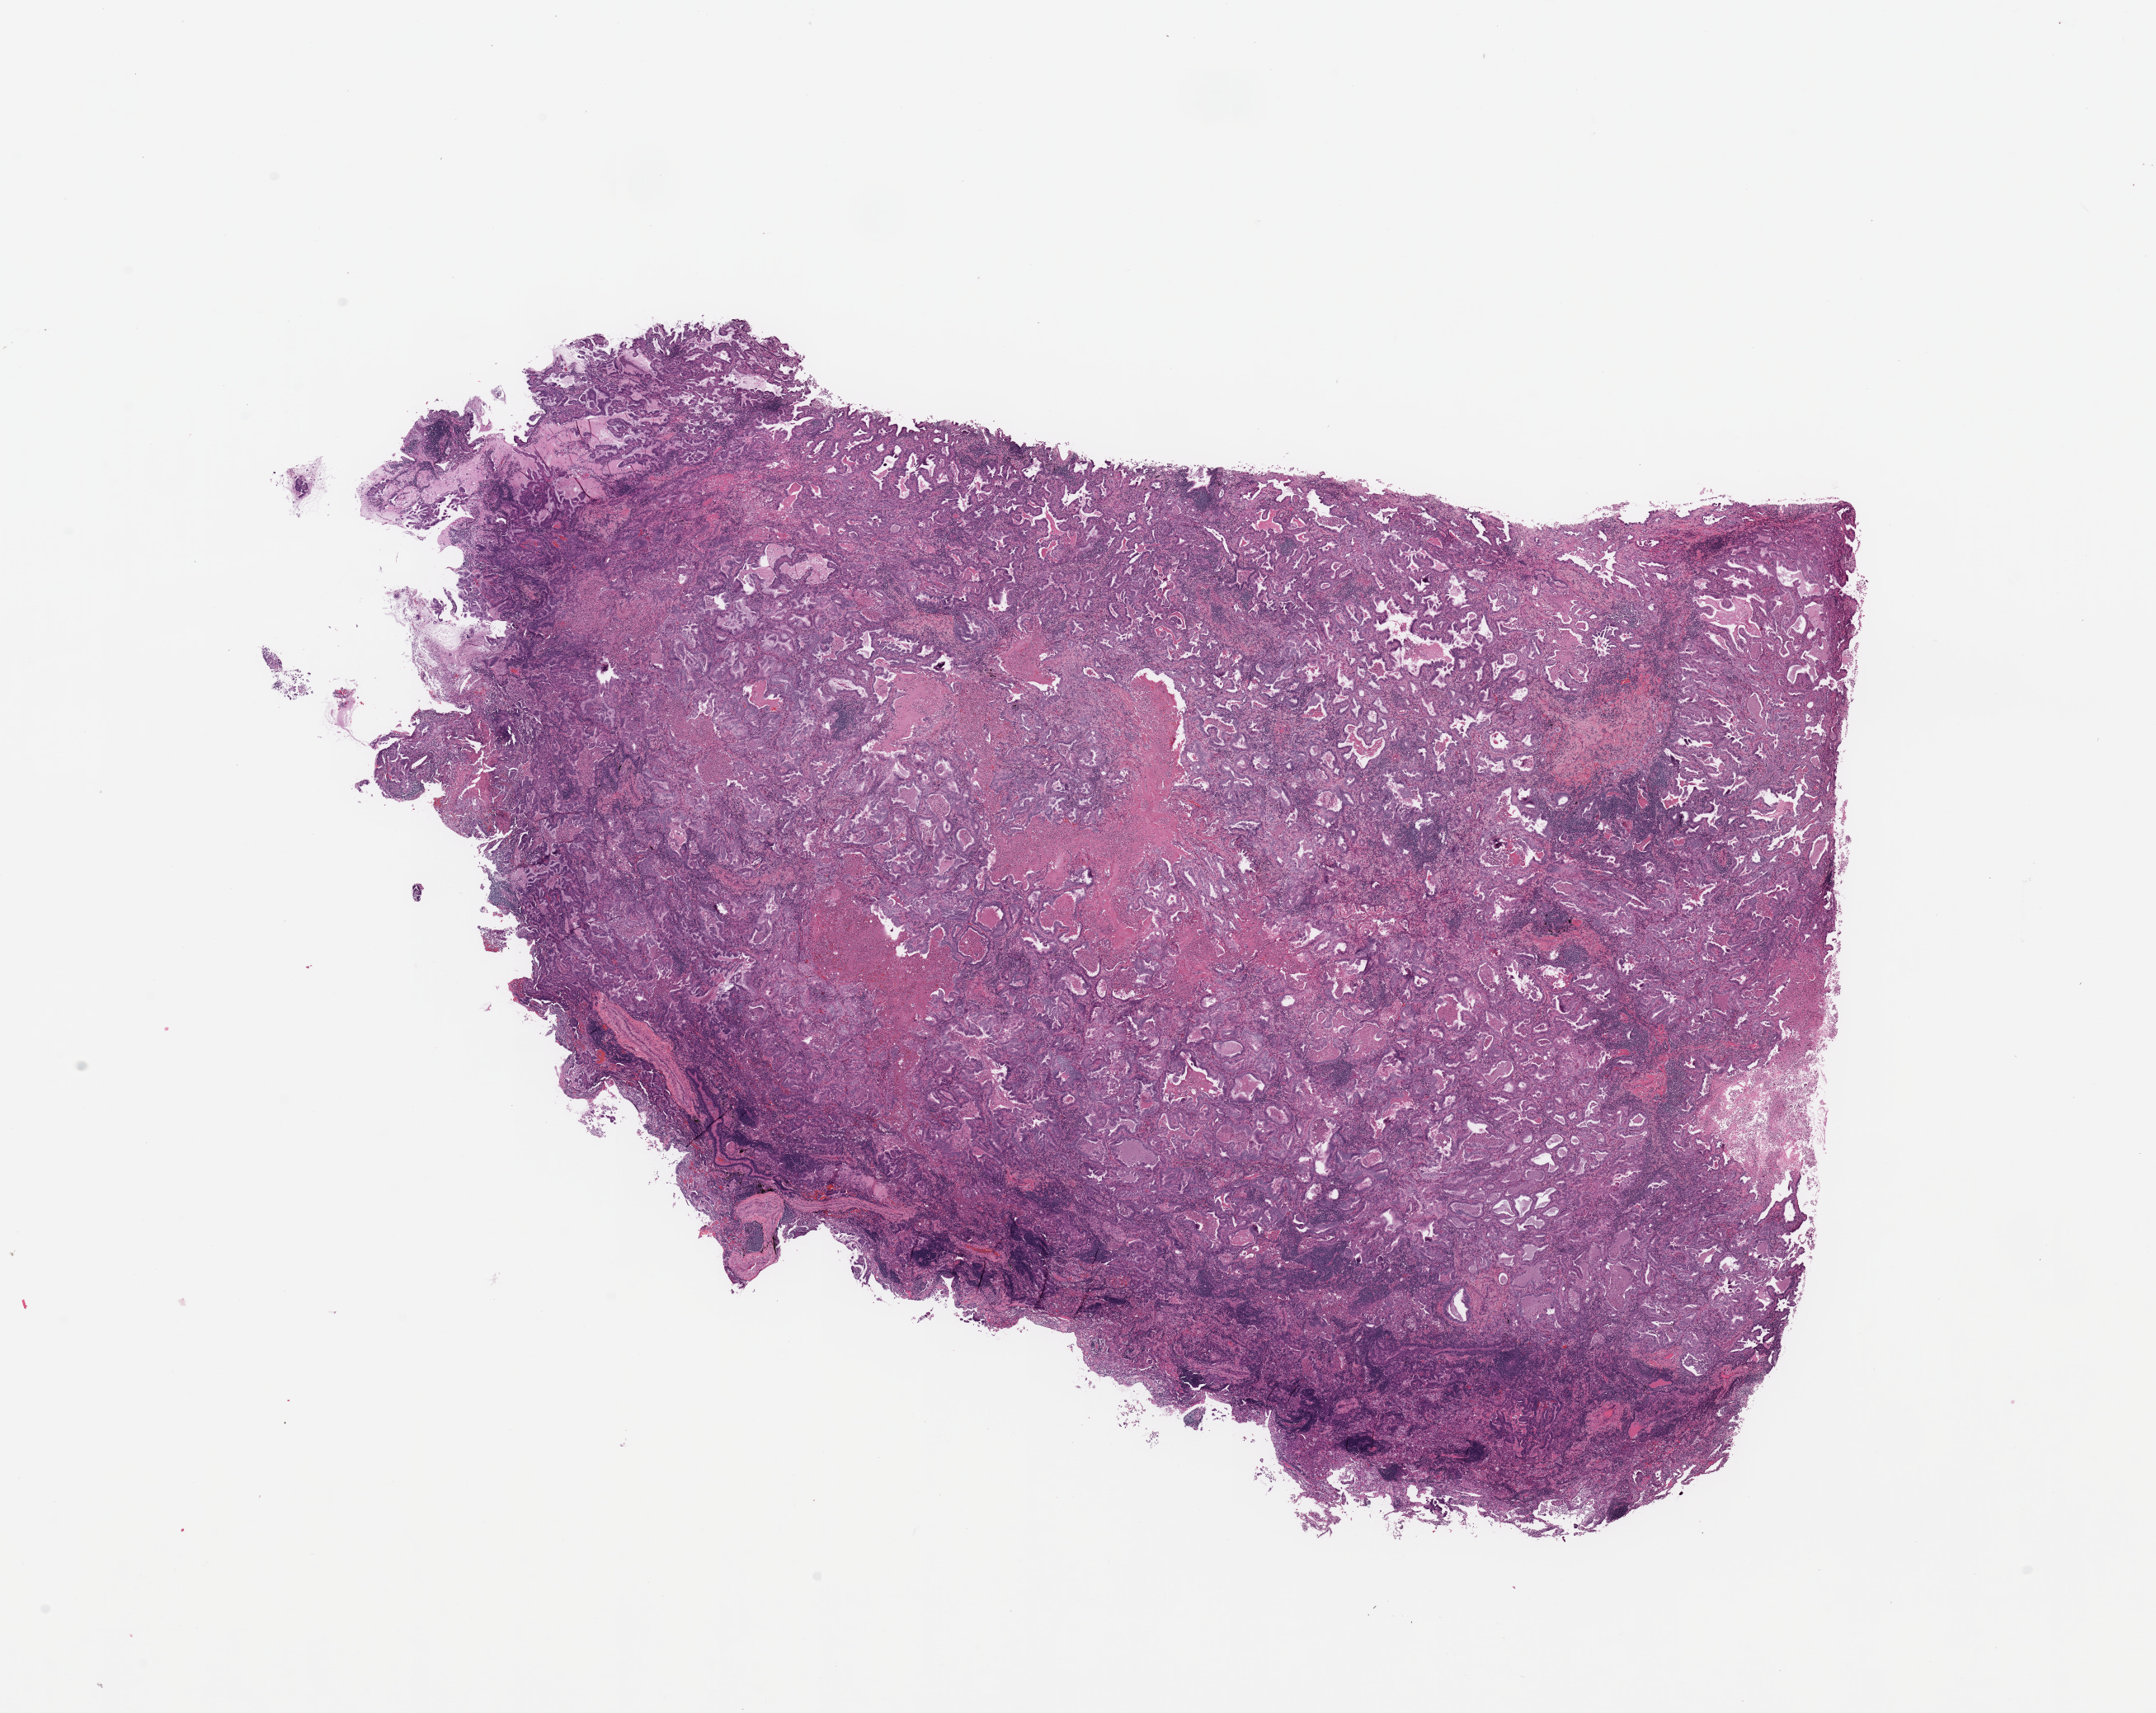
Hematoxylin and eosin (H&E) stained whole-slide image — low-resolution overview of the scanned area, about 20.7 x 16.4 mm. Lung, tumour tissue. 76-year-old male patient. Histologic grade: G2 (moderately differentiated).
• histologic diagnosis: Adenocarcinoma, NOS
• AJCC pathologic stage: IB
• primary tumour site (as recorded): right lower lobe